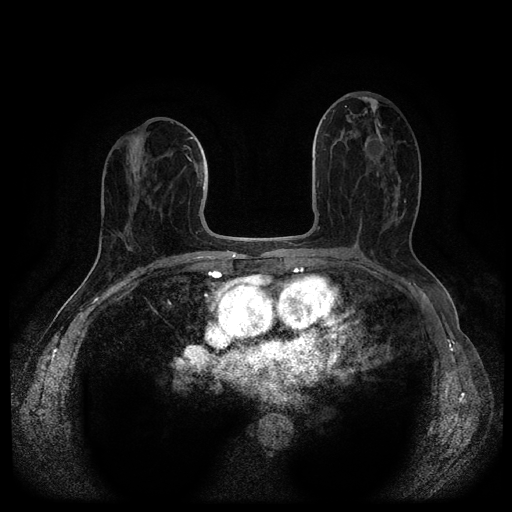
Breast MRI (dynamic contrast-enhanced, multi-phase), one axial slice. Dynamic contrast-enhanced series, time point 2 of 5 at this slice position (early post-contrast). 1.5 T. TE 2.6 ms, TR 5.4 ms. 2.1 mm slice thickness. 512 × 512 image matrix. Female patient, age 69 years.
Annotated regions visible in this slice (semi-automatic segmentation, software-assisted and operator-edited):
- breast lesion (labelled benign in the annotation): box from (x=364, y=136) to (x=387, y=161) px